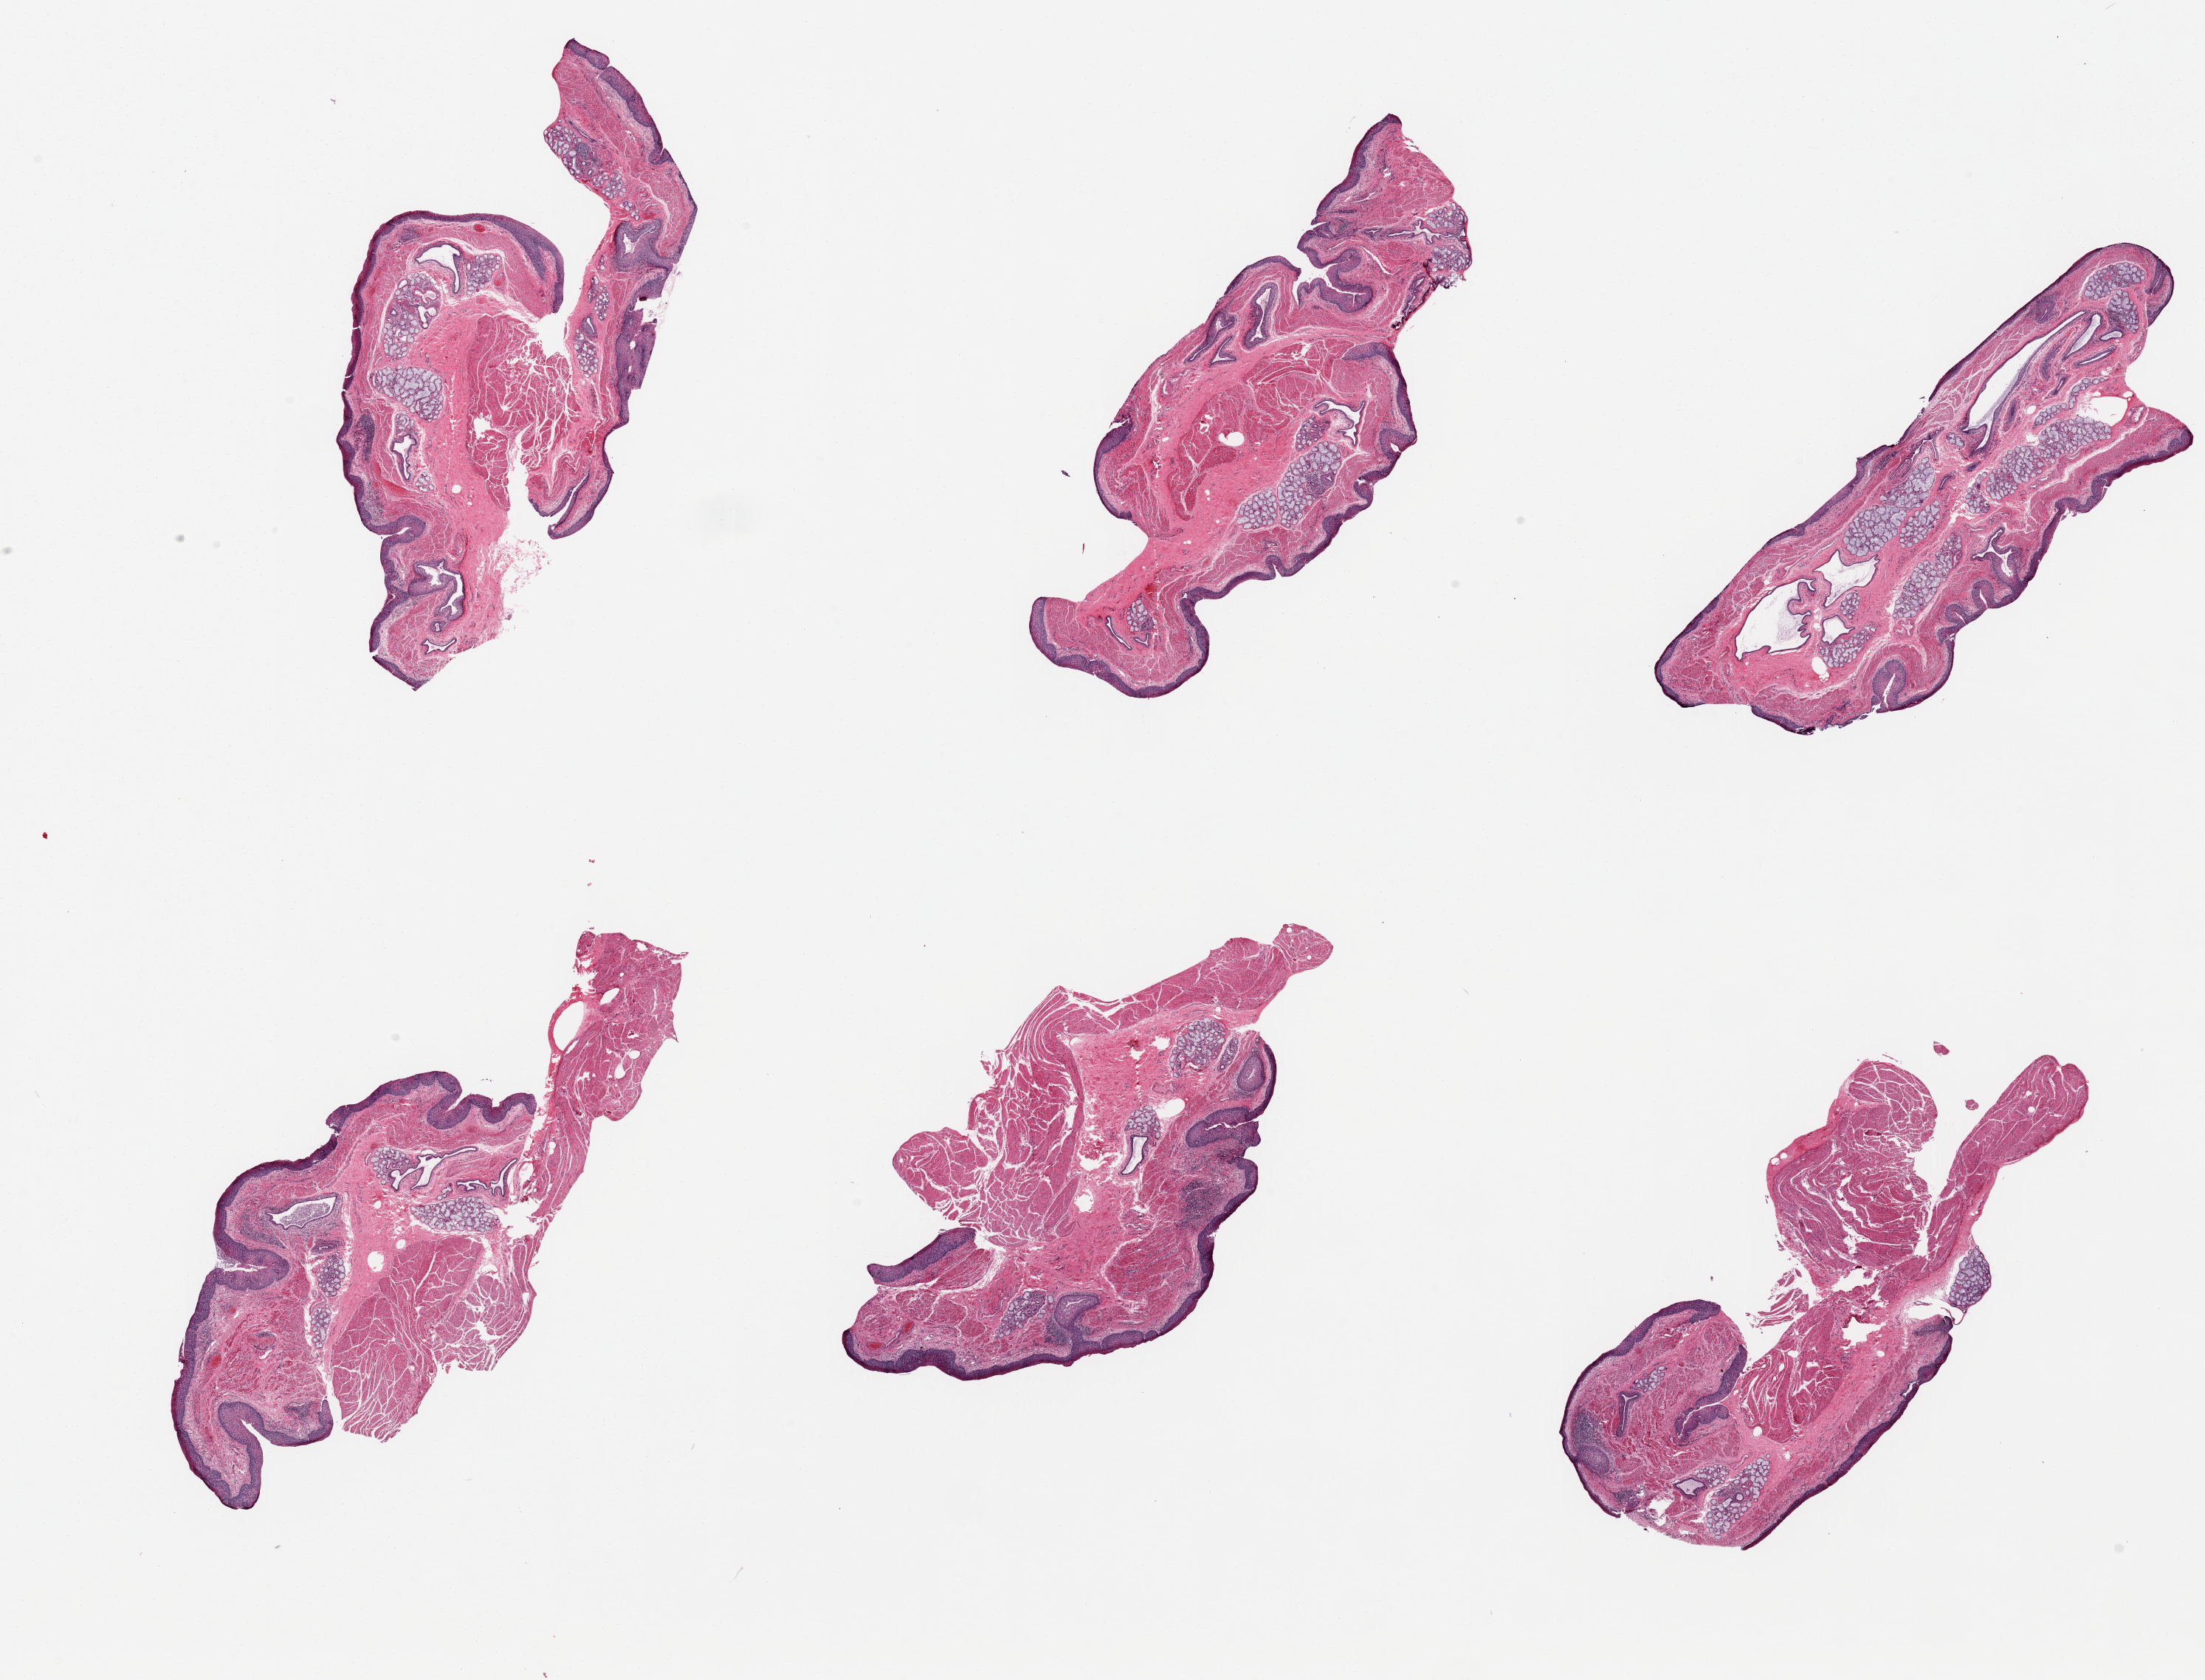
Whole-slide image, hematoxylin and eosin (H&E) stain — whole scanned area (about 23.6 x 18.0 mm, from a 20x scan) shown as a low-resolution overview. PAXgene-fixed paraffin-embedded (PFPE) section. Sampled site (target tissue): esophageal mucous membrane. Tissue donor sample. Male donor.
Pathologist's review note for this sample: 6 pieces, squamous mucosa up to ~0.2 mm; abundant submucosal mucus glands.